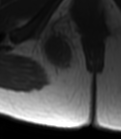
MRI of an extremity soft-tissue mass, one axial slice. Slice 29 of 47 in the series (ordered by position). MR volume resampled by the dataset authors to the PET/CT grid (not the native acquisition matrix). 3.27 mm slice thickness. 121 × 139 image matrix, field of view 118 × 136 mm. Female patient. From the clinical record (not read from this slice): histological type: epithelioid sarcoma; grade: intermediate; site of the primary tumour: right buttock.
Outlined on this slice (expert contour drawn on MRI and transferred to this co-registered scan by the dataset authors):
- gross tumour volume including surrounding oedema: bounding box (x1, y1, x2, y2) in pixels: (36, 25, 80, 76)
- gross tumour volume (mass): (39, 34, 73, 71)